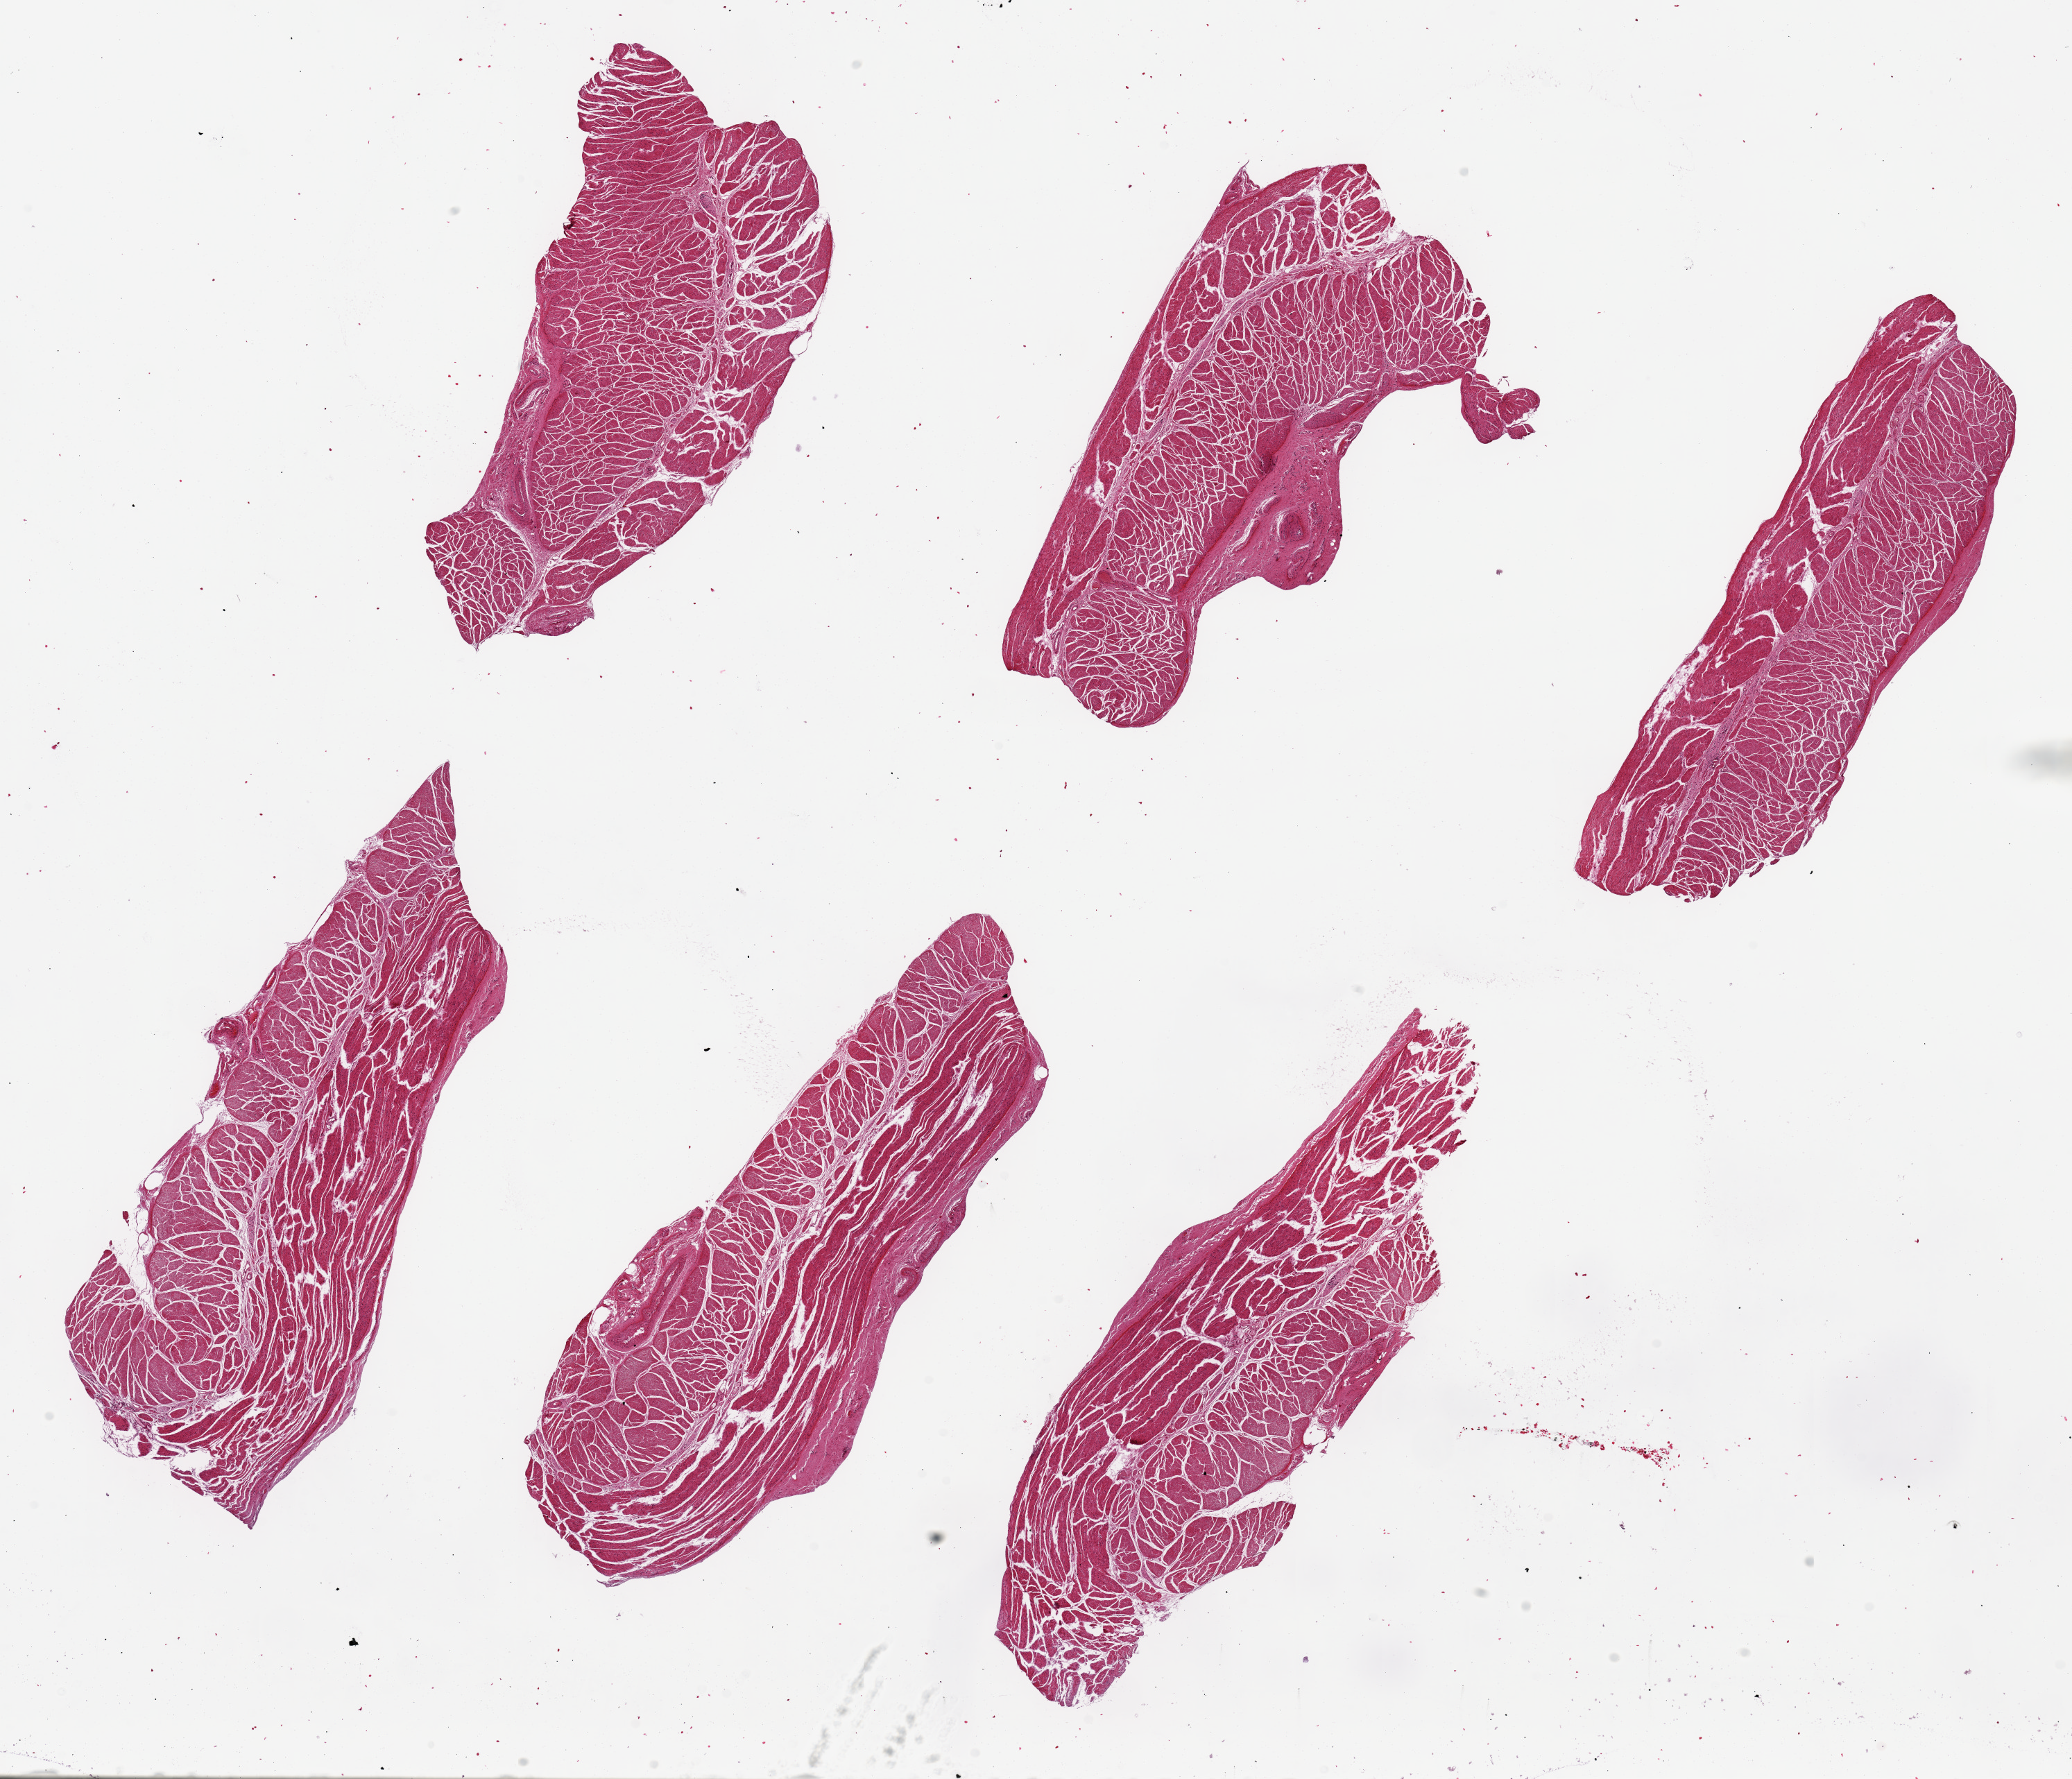
H&E whole-slide image — shown as a low-resolution overview of the whole scanned area (about 23.6 x 20.3 mm, slide scanned at 20x). PAXgene-fixed paraffin-embedded (PFPE) section. Section of esophageal muscle (target tissue). Donor tissue sample. Donor: male.
Pathologist's review note for this sample: 6 pieces up to 8x3 mm; good clean muscular specimens.